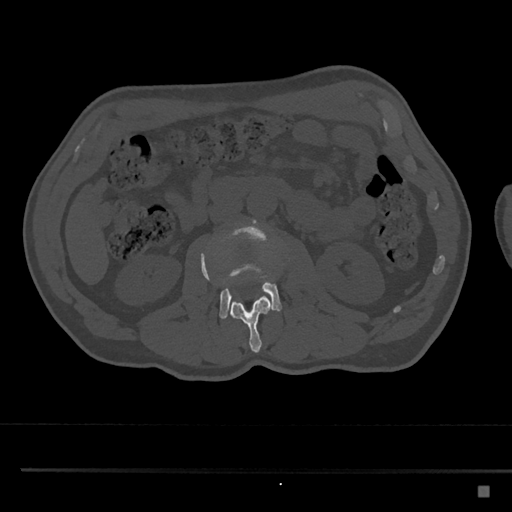
CT including the spine, one axial slice; slice 731 of 797 in the series (ordered by position); reconstruction kernel Br40s/3; bone window (W 1800 / L 400 HU); 0.5 mm slice thickness; 512 × 512 image matrix, field of view 391 × 391 mm. Patient: male, 59 years. Case-level facts recorded for this patient, not image findings: primary cancer: prostate.
Structures marked on this image (semi-automatically segmented with operator editing):
- L2 vertebra: box from (x=201, y=253) to (x=272, y=353) px
- L3 vertebra: (x=201, y=219)–(x=289, y=320)